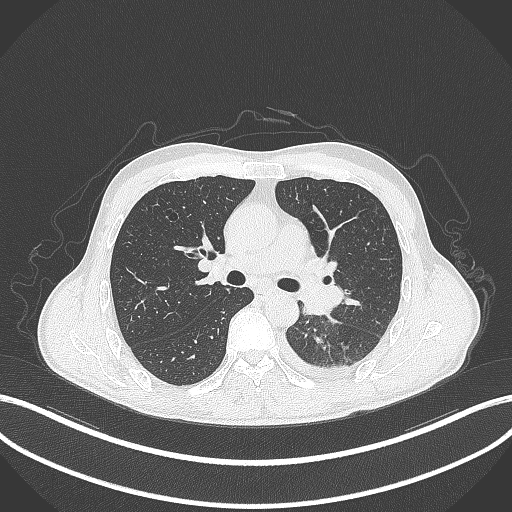
Chest CT, one axial slice; slice 197 of 295 in the series (ordered by position); reconstruction kernel B70f; 120 kVp; lung window (W 1500 / L -600 HU); 1 mm slice thickness; 512 × 512 image matrix, field of view 400 × 400 mm. Male patient, age 47 years. From the clinical record (not read from this slice): clinical TNM (as recorded): T3 N1 M1c; histopathological grade: G3.
Outlined on this slice (rectangle marked by the reading radiologist):
- lung tumour (recorded histology: small cell carcinoma): bounding box <299,275,345,316> (left, top, right, bottom; pixels)